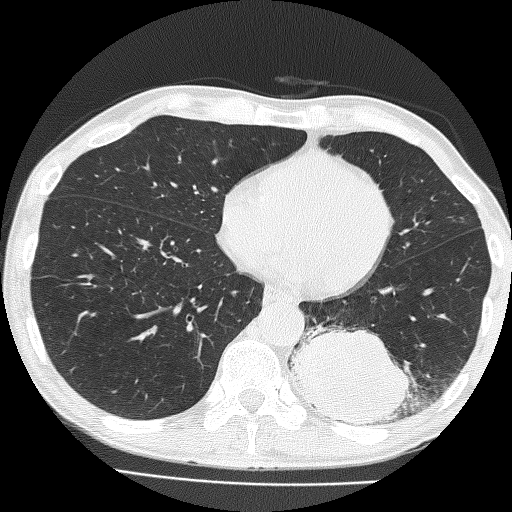
Low-dose screening chest CT, one axial slice; position 61 of 160 along the scan axis; lung window (W 1500 / L -600 HU); 2 mm slice thickness; 512 × 512 image matrix, field of view 324 × 324 mm.
Outlined on this slice (outlined manually by an expert reader):
- lesion 1 (tumor, lower lobe of left lung): bounding box <292,327,412,425> (left, top, right, bottom; pixels)